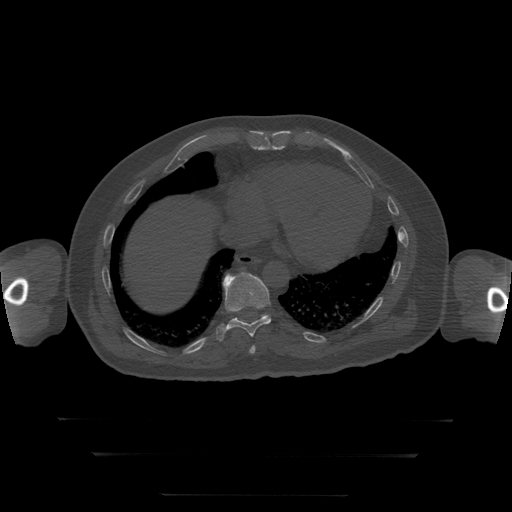
CT including the spine, one axial slice. Position 121 of 397 along the scan axis. Reconstruction kernel STANDARD. 120 kVp. Bone window (W 1800 / L 400 HU). 512 × 512 image matrix, field of view 510 × 510 mm. Patient age 73 years. Case-level facts recorded for this patient, not image findings: primary cancer: prostate.
Annotated regions visible in this slice (semi-automatically segmented with operator editing):
- T10 vertebra: box from (x=216, y=272) to (x=272, y=342) px
- T9 vertebra: (x=249, y=346)–(x=256, y=354)